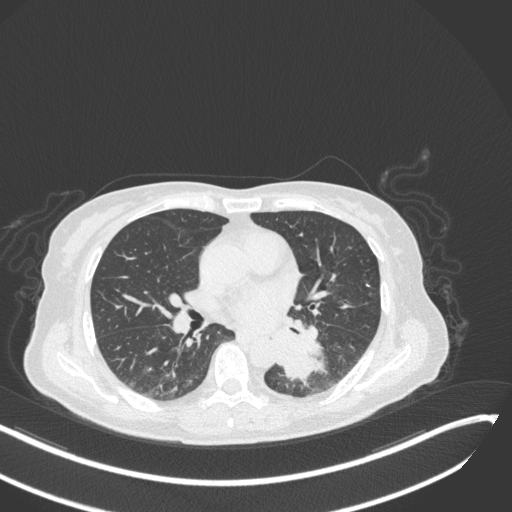
Chest CT, one axial slice. Position 138 of 342 along the scan axis. 120 kVp. Lung window (W 1500 / L -600 HU). 1 mm slice thickness. 512 × 512 image matrix, field of view 400 × 400 mm. Female patient, age 64 years. From the clinical record (not read from this slice): clinical TNM (as recorded): T3 N1 M1; histopathological grade: G3.
Annotated regions visible in this slice (bounding box drawn by a radiologist):
- lung tumour (recorded histology: small cell carcinoma): bounding box <276,333,330,391> (left, top, right, bottom; pixels)